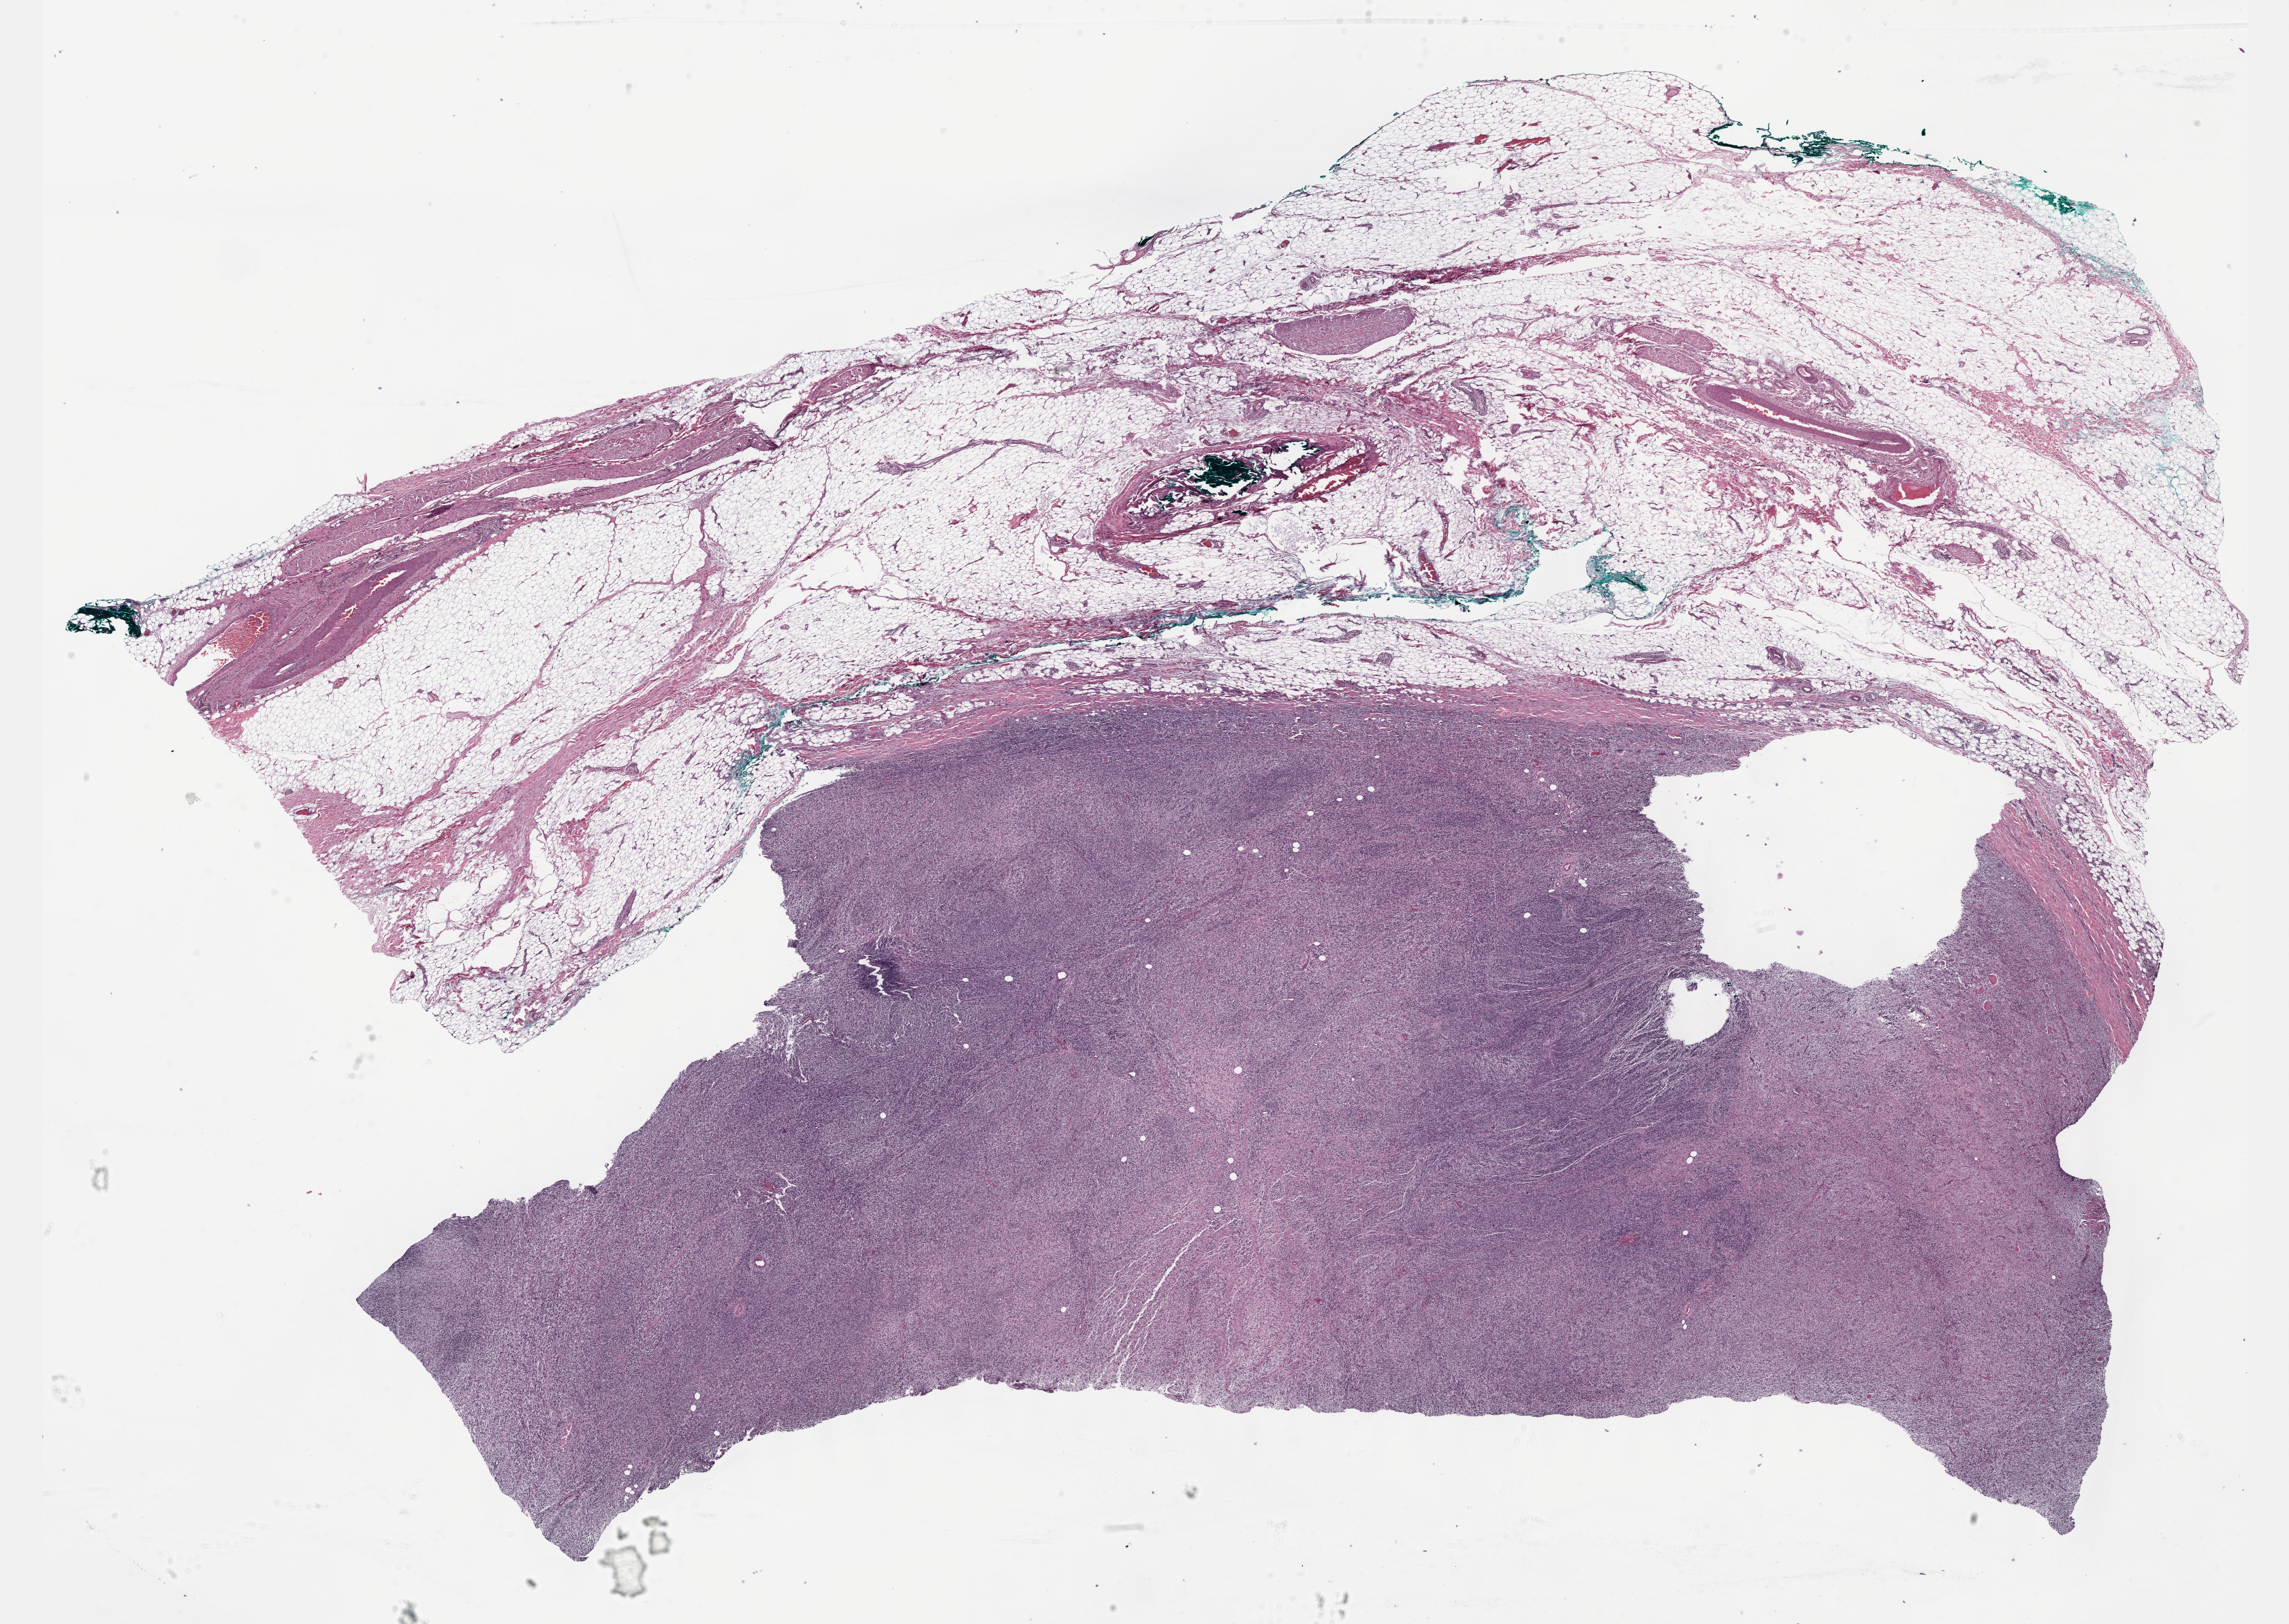
Whole-slide histology image, H&E-stained — a low-resolution overview of the entire scanned area, about 27.2 x 19.3 mm (slide scanned at 40x); FFPE section; connective, subcutaneous and other soft tissues, primary tumour sample. Female, age 34 years at initial diagnosis.
• diagnosis: Malignant peripheral nerve sheath tumor (connective, subcutaneous and other soft tissues of thorax)